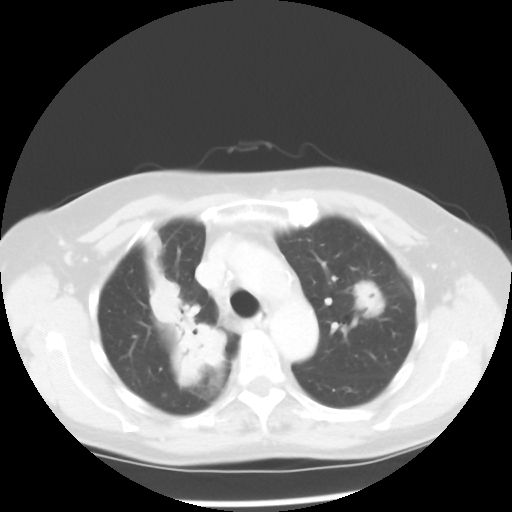
Chest CT, one axial slice; slice 37 of 52 in the series (ordered by position); reconstruction kernel STANDARD; lung window (W 1500 / L -600 HU); 512 × 512 image matrix. Patient: female, 60 years. From the clinical record (not read from this slice): clinical TNM (as recorded): T2 N1 M1a.
Annotated regions visible in this slice (bounding box drawn by a radiologist):
- lung tumour (recorded histology: adenocarcinoma): bounding box (x1, y1, x2, y2) in pixels: (136, 256, 237, 393)